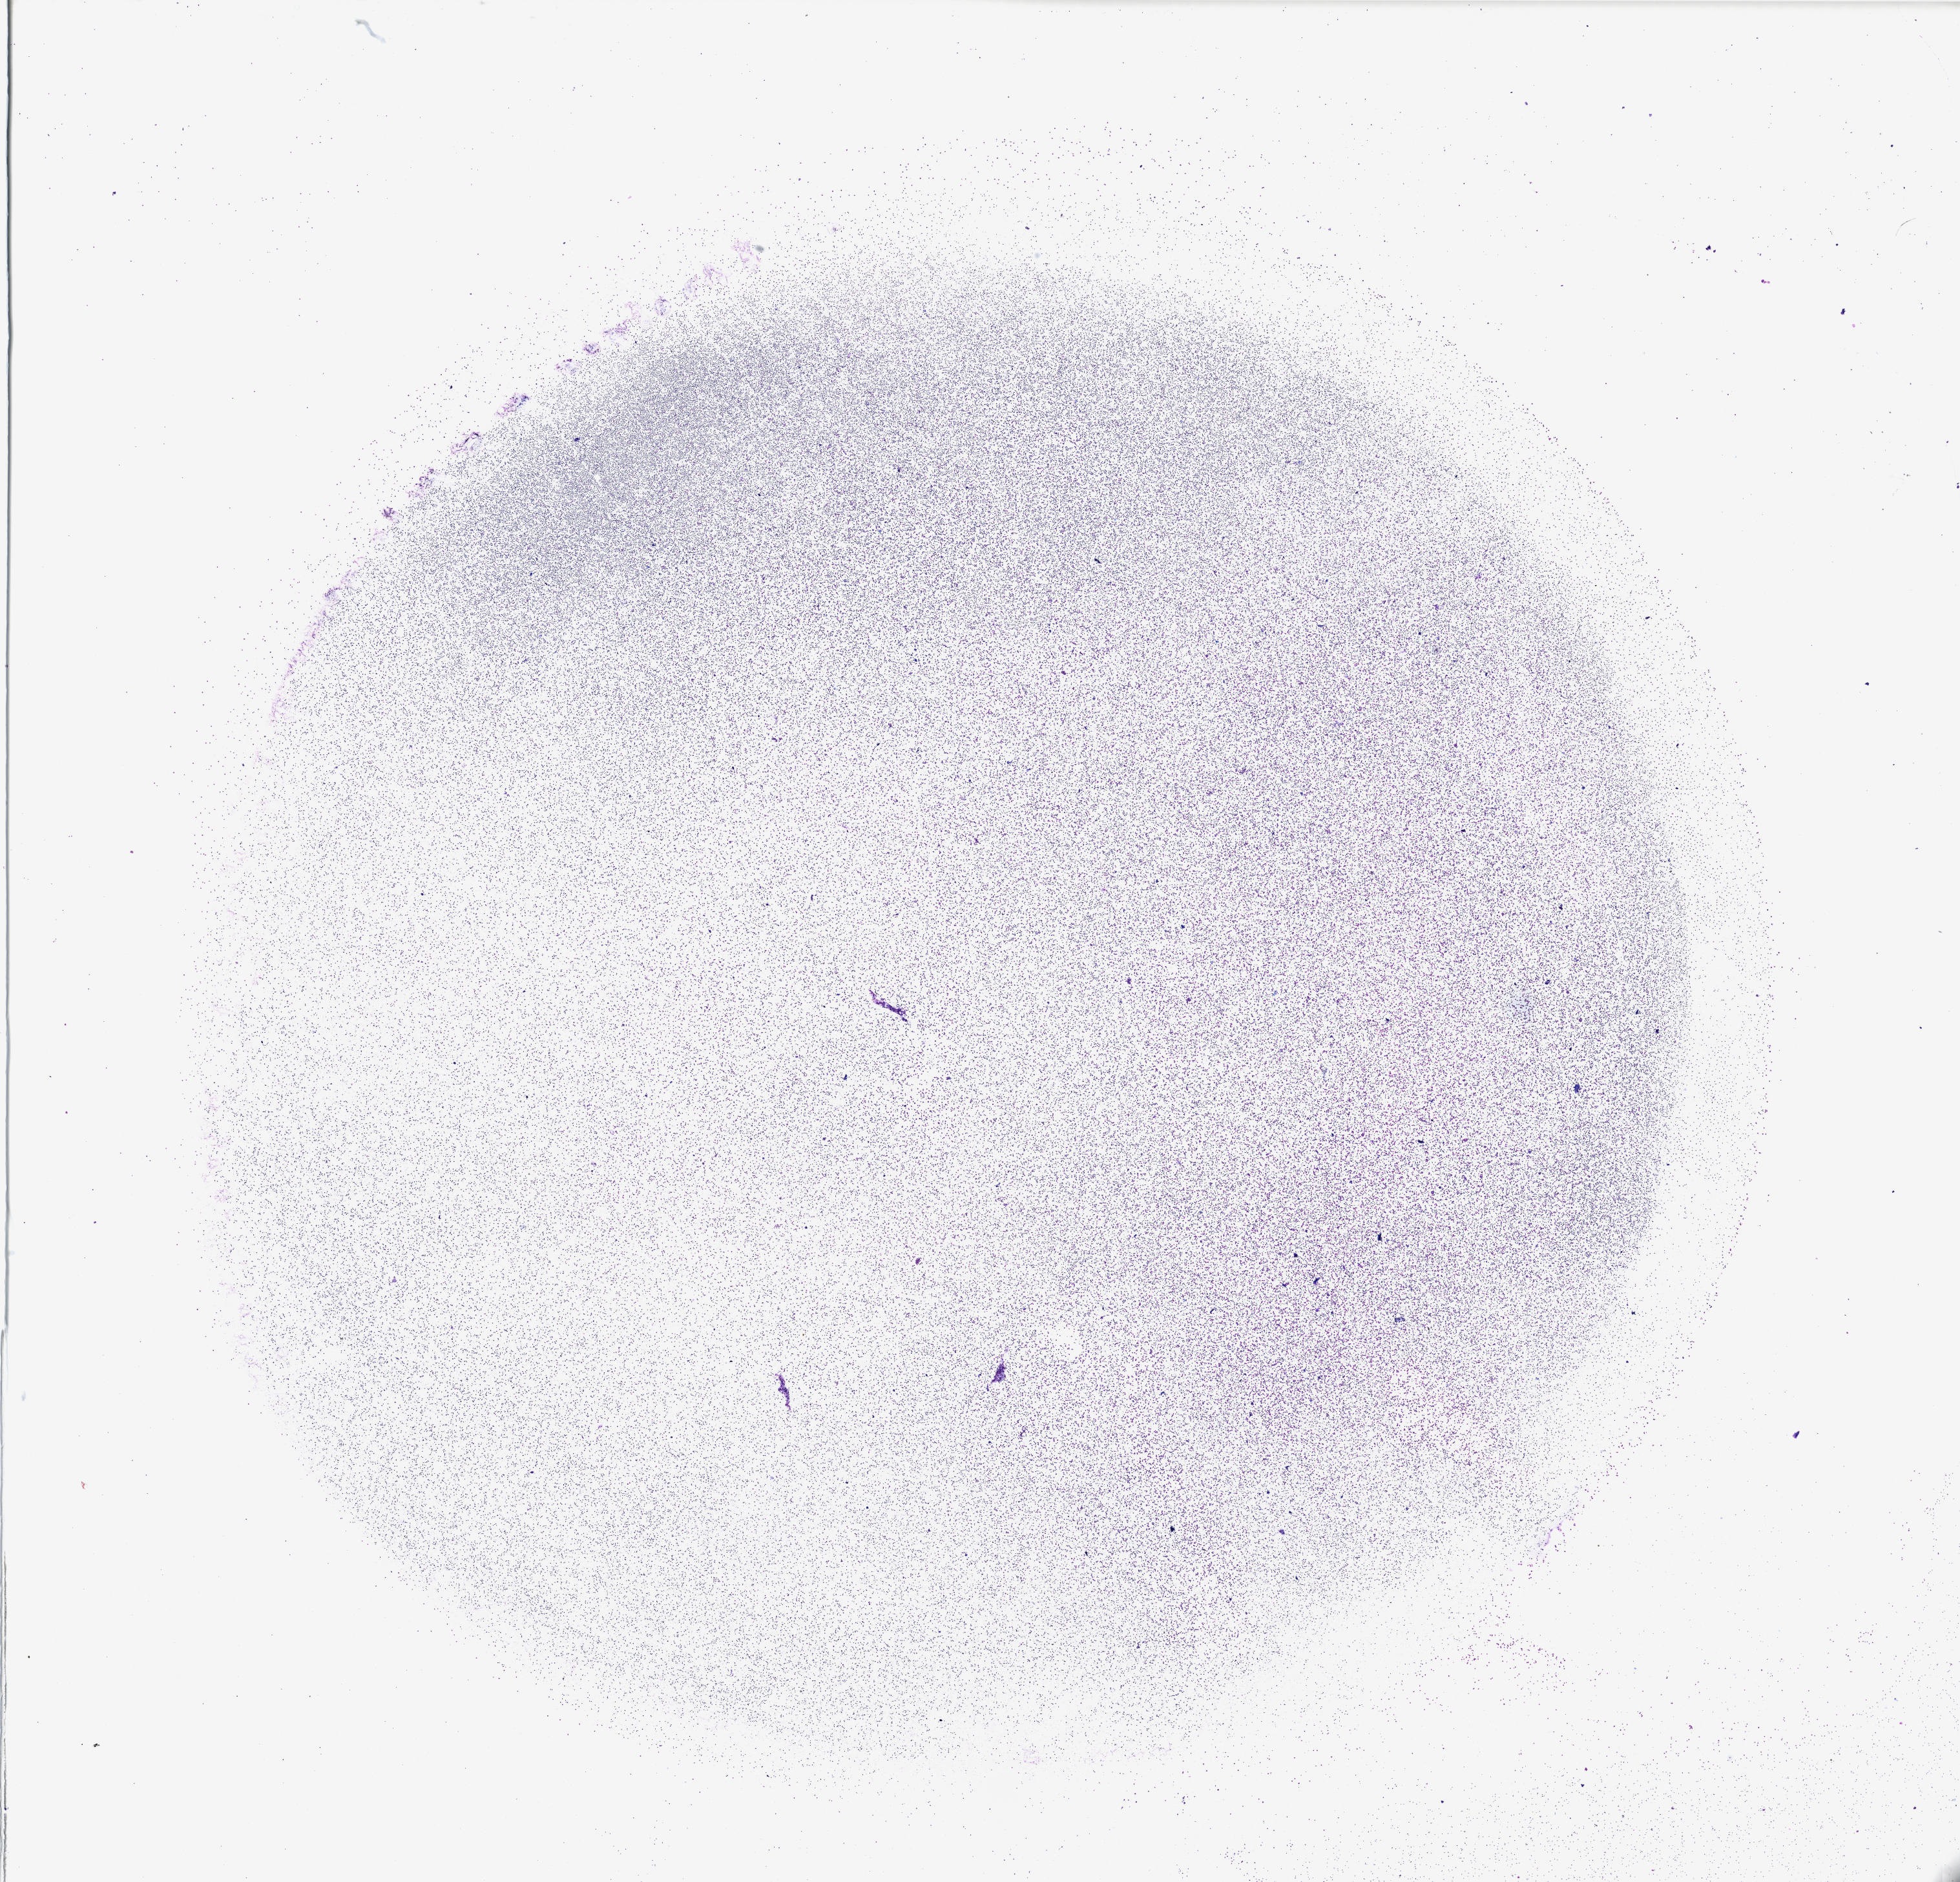
Whole-slide histology image, H&E — a low-resolution overview of the entire scanned area, about 24.0 x 23.0 mm, bone marrow (leukaemic) sample. 59-year-old male patient. Blasts: 90%.
• FAB classification: M1
• diagnosis: Acute Myeloid Leukemia
• WHO classification: AML without maturation